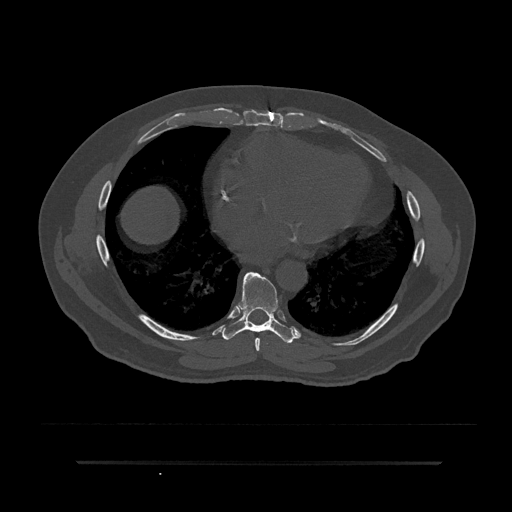
CT including the spine, one axial slice. Position 439 of 797 along the scan axis. Reconstruction kernel Br40s/3. Bone window (W 1800 / L 400 HU). 0.5 mm slice thickness. 512 × 512 image matrix, field of view 464 × 464 mm. Patient: male, 59 years. From the clinical record (not read from this slice): primary cancer: bile ducts.
Outlined on this slice (semi-automatically segmented with operator editing):
- T7 vertebra: box from (x=255, y=338) to (x=260, y=352) px
- T8 vertebra: (x=222, y=272)–(x=295, y=343)